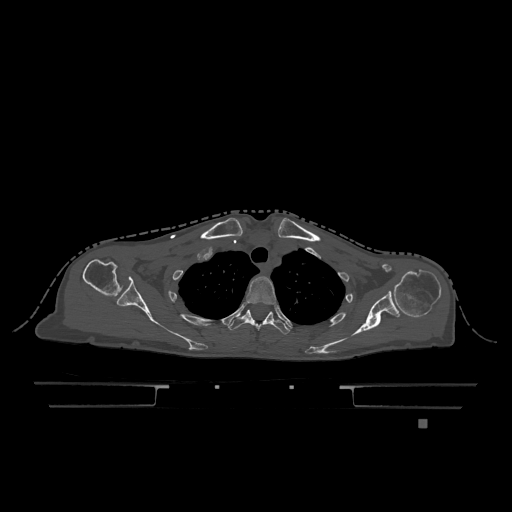
CT including the spine, one axial slice. Position 942 of 1317 along the scan axis. Bone window (W 1800 / L 400 HU). 512 × 512 image matrix, field of view 500 × 500 mm. Female patient, age 74 years. From the clinical record (not read from this slice): primary cancer: lung.
Annotated regions visible in this slice (semi-automatically segmented with operator editing):
- T2 vertebra: bounding box (x1, y1, x2, y2) in pixels: (246, 276, 276, 305)
- T3 vertebra: (229, 310, 290, 335)
- T6 vertebra: (270, 312, 273, 314)